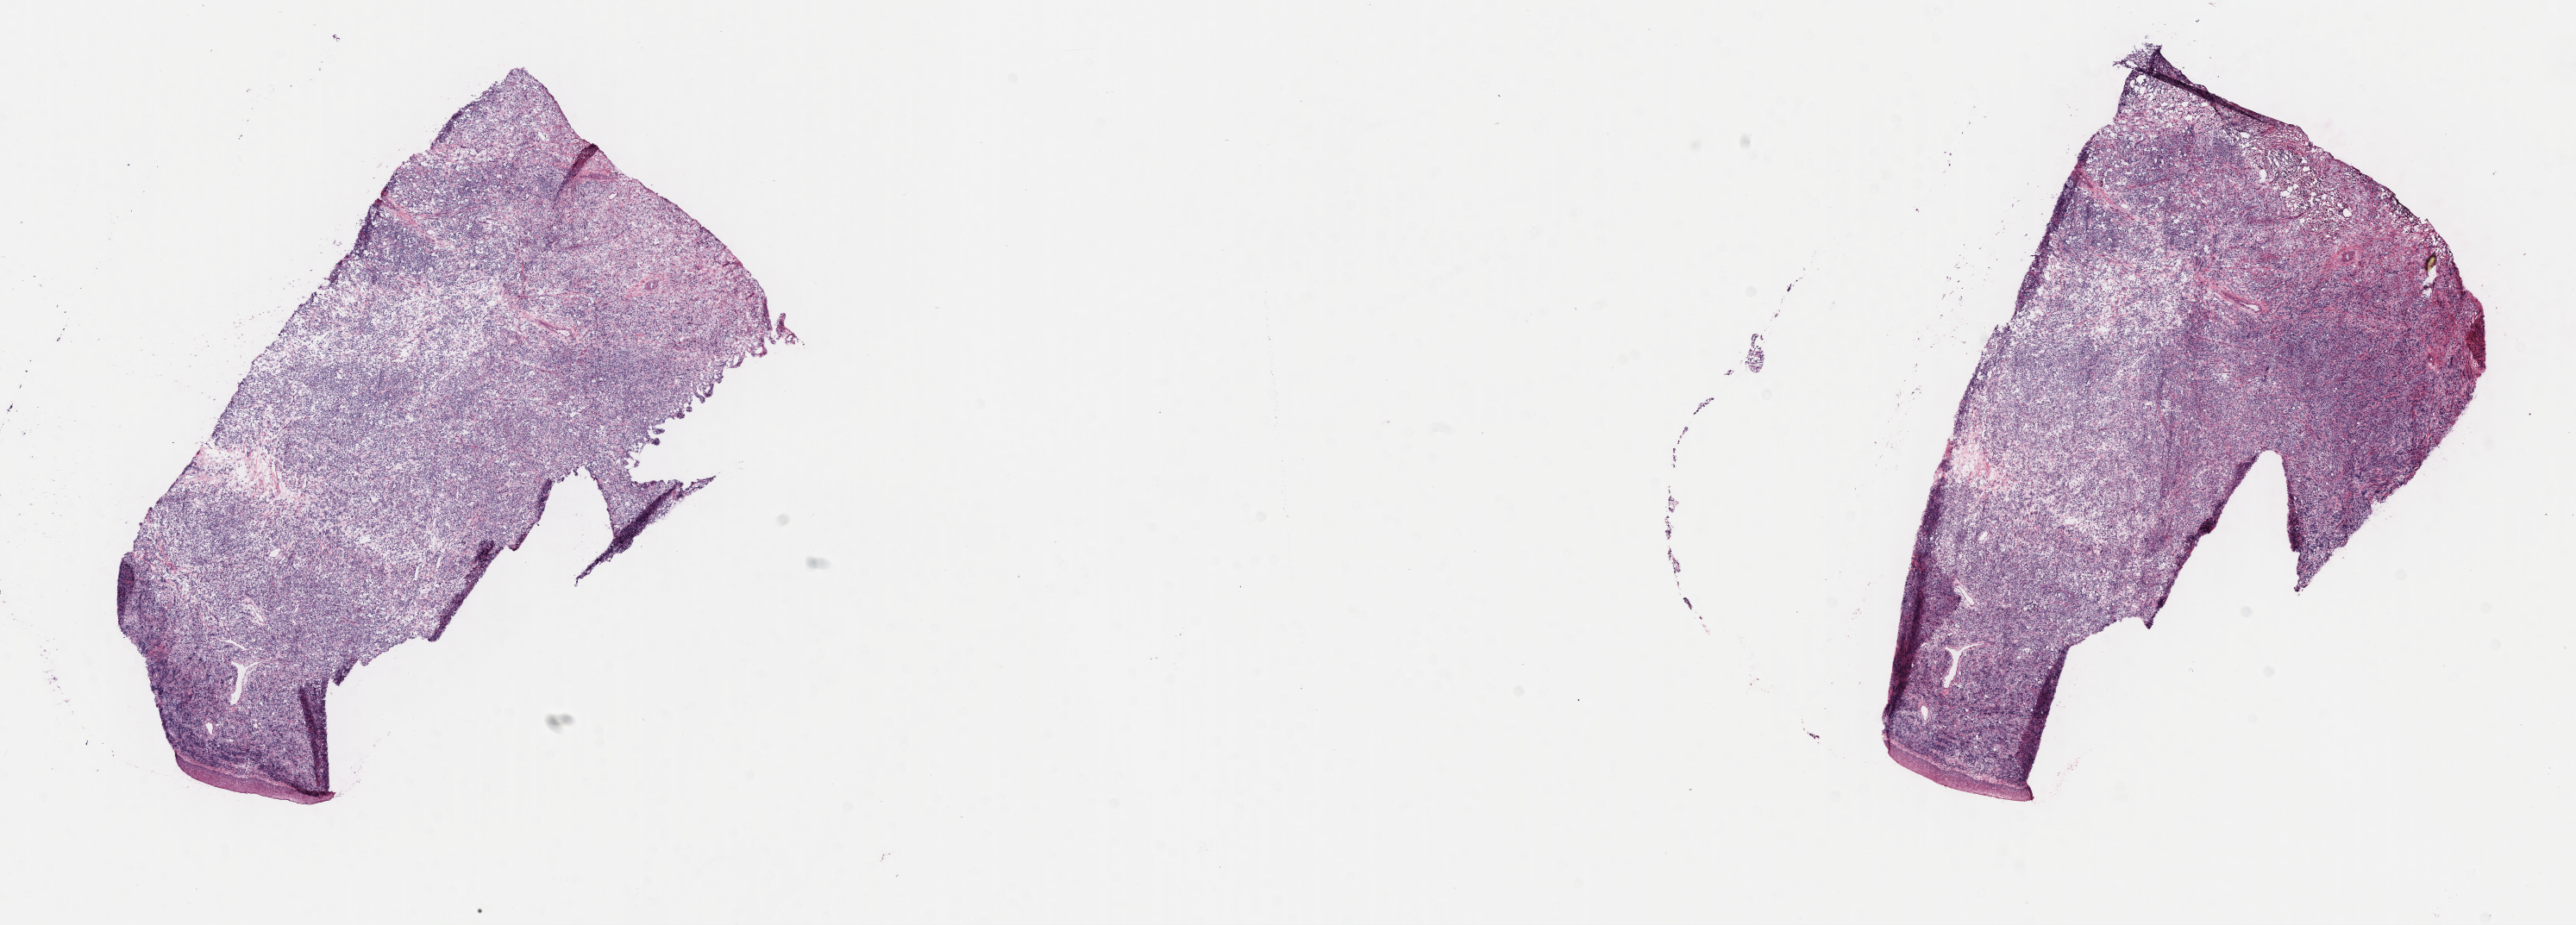
Digitized H&E-stained section, shown as a low-resolution overview of the whole scanned area (about 24.2 x 8.7 mm). Cryosection. Specimen: primary tumor. Anatomic site: cranium. Male patient; age at initial diagnosis 5 years. Composition of this section per pathologist review: tumor cells 93%, tumor nuclei 90%, stromal cells 5%, necrosis 2%, normal cells 0%. Infiltration values recorded for this section: lymphocyte infiltration 2%, monocyte infiltration 3%, neutrophil infiltration 0%.
Diagnosis: Diffuse large B-cell lymphoma, NOS. Ann Arbor stage (patient): Stage IV. Section: bottom of the tissue portion.